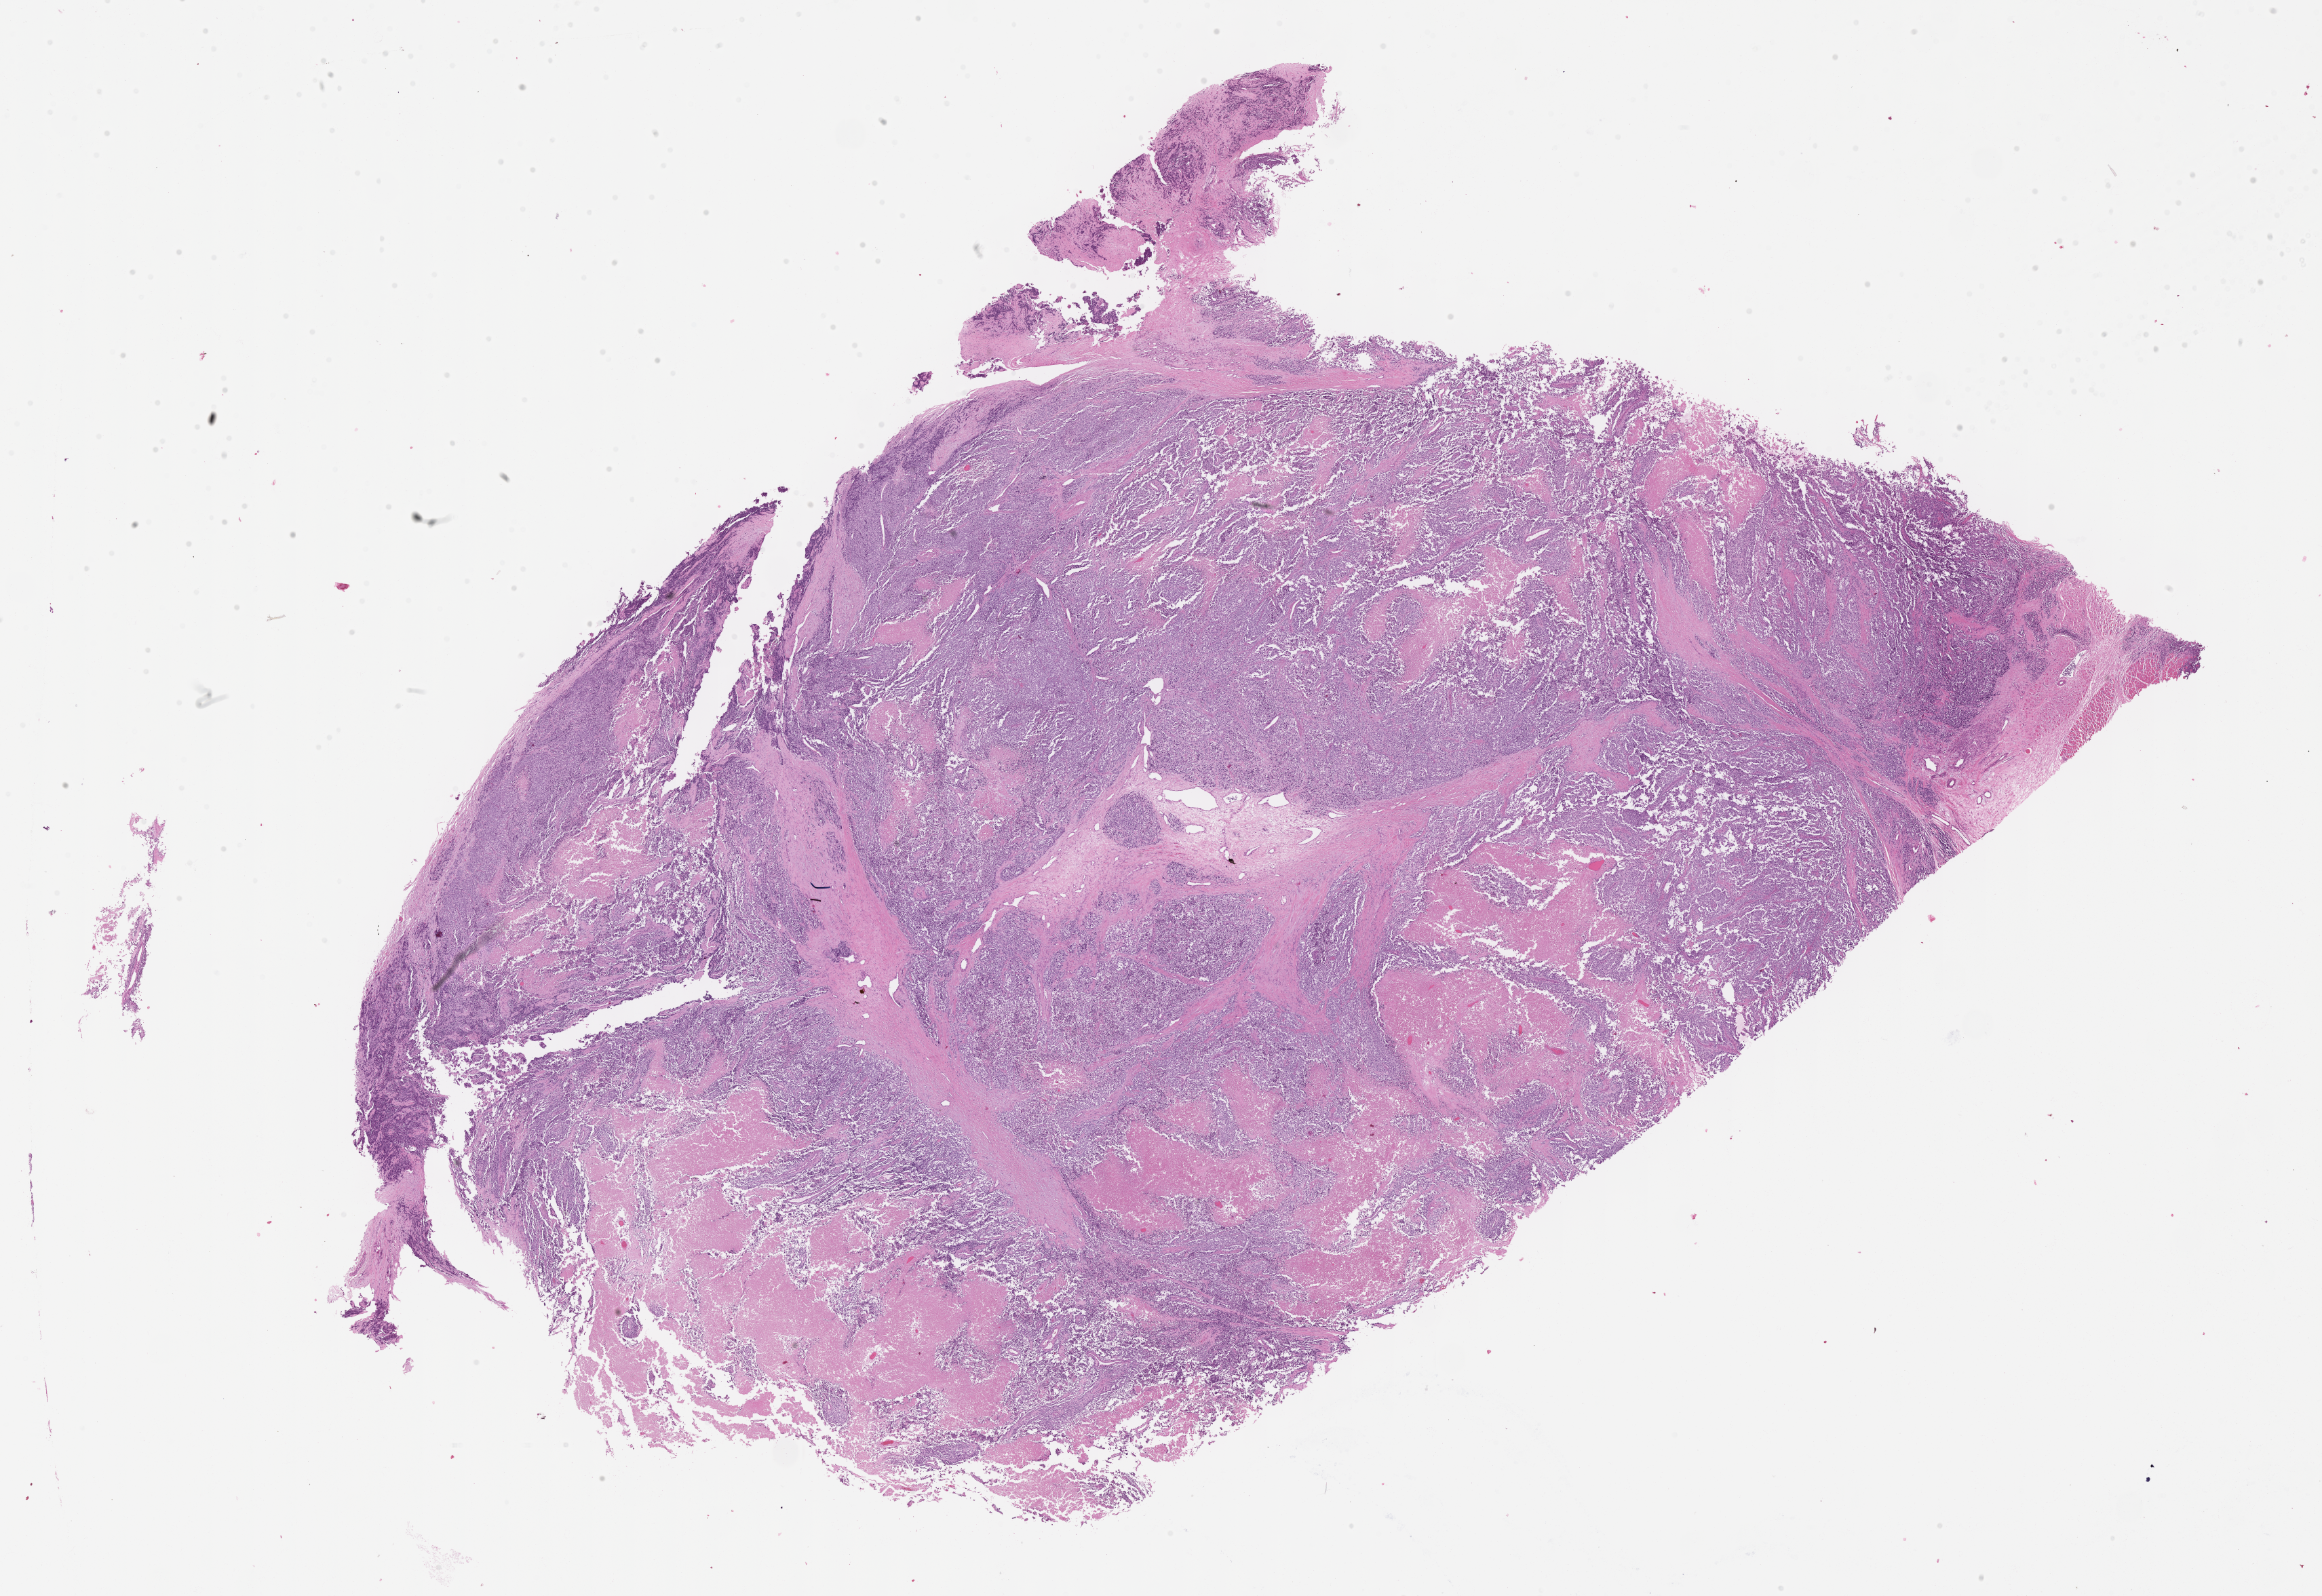
Digitized hematoxylin and eosin (H&E)-stained section of tumor tissue — low-resolution overview of the scanned area, about 27.7 x 19.0 mm, formalin-fixed, paraffin-embedded (FFPE) tissue, site: thigh mass, right. Male patient, age at diagnosis 10.5 years.
Diagnosis: rhabdomyosarcoma; histological classification: alveolar rhabdomyosarcoma.